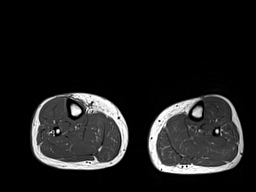
MRI of an extremity soft-tissue mass, one axial slice. Position 10 of 32 along the scan axis. 6 mm slice thickness. 256 × 192 image matrix. Female patient. Case-level facts recorded for this patient, not image findings: histological type: undifferentiated – high grade; grade: high; site of the primary tumour: right thigh.
Structures marked on this image (manually delineated by an expert):
- gross tumour volume (mass): bounding box (x1, y1, x2, y2) in pixels: (76, 99, 85, 107)